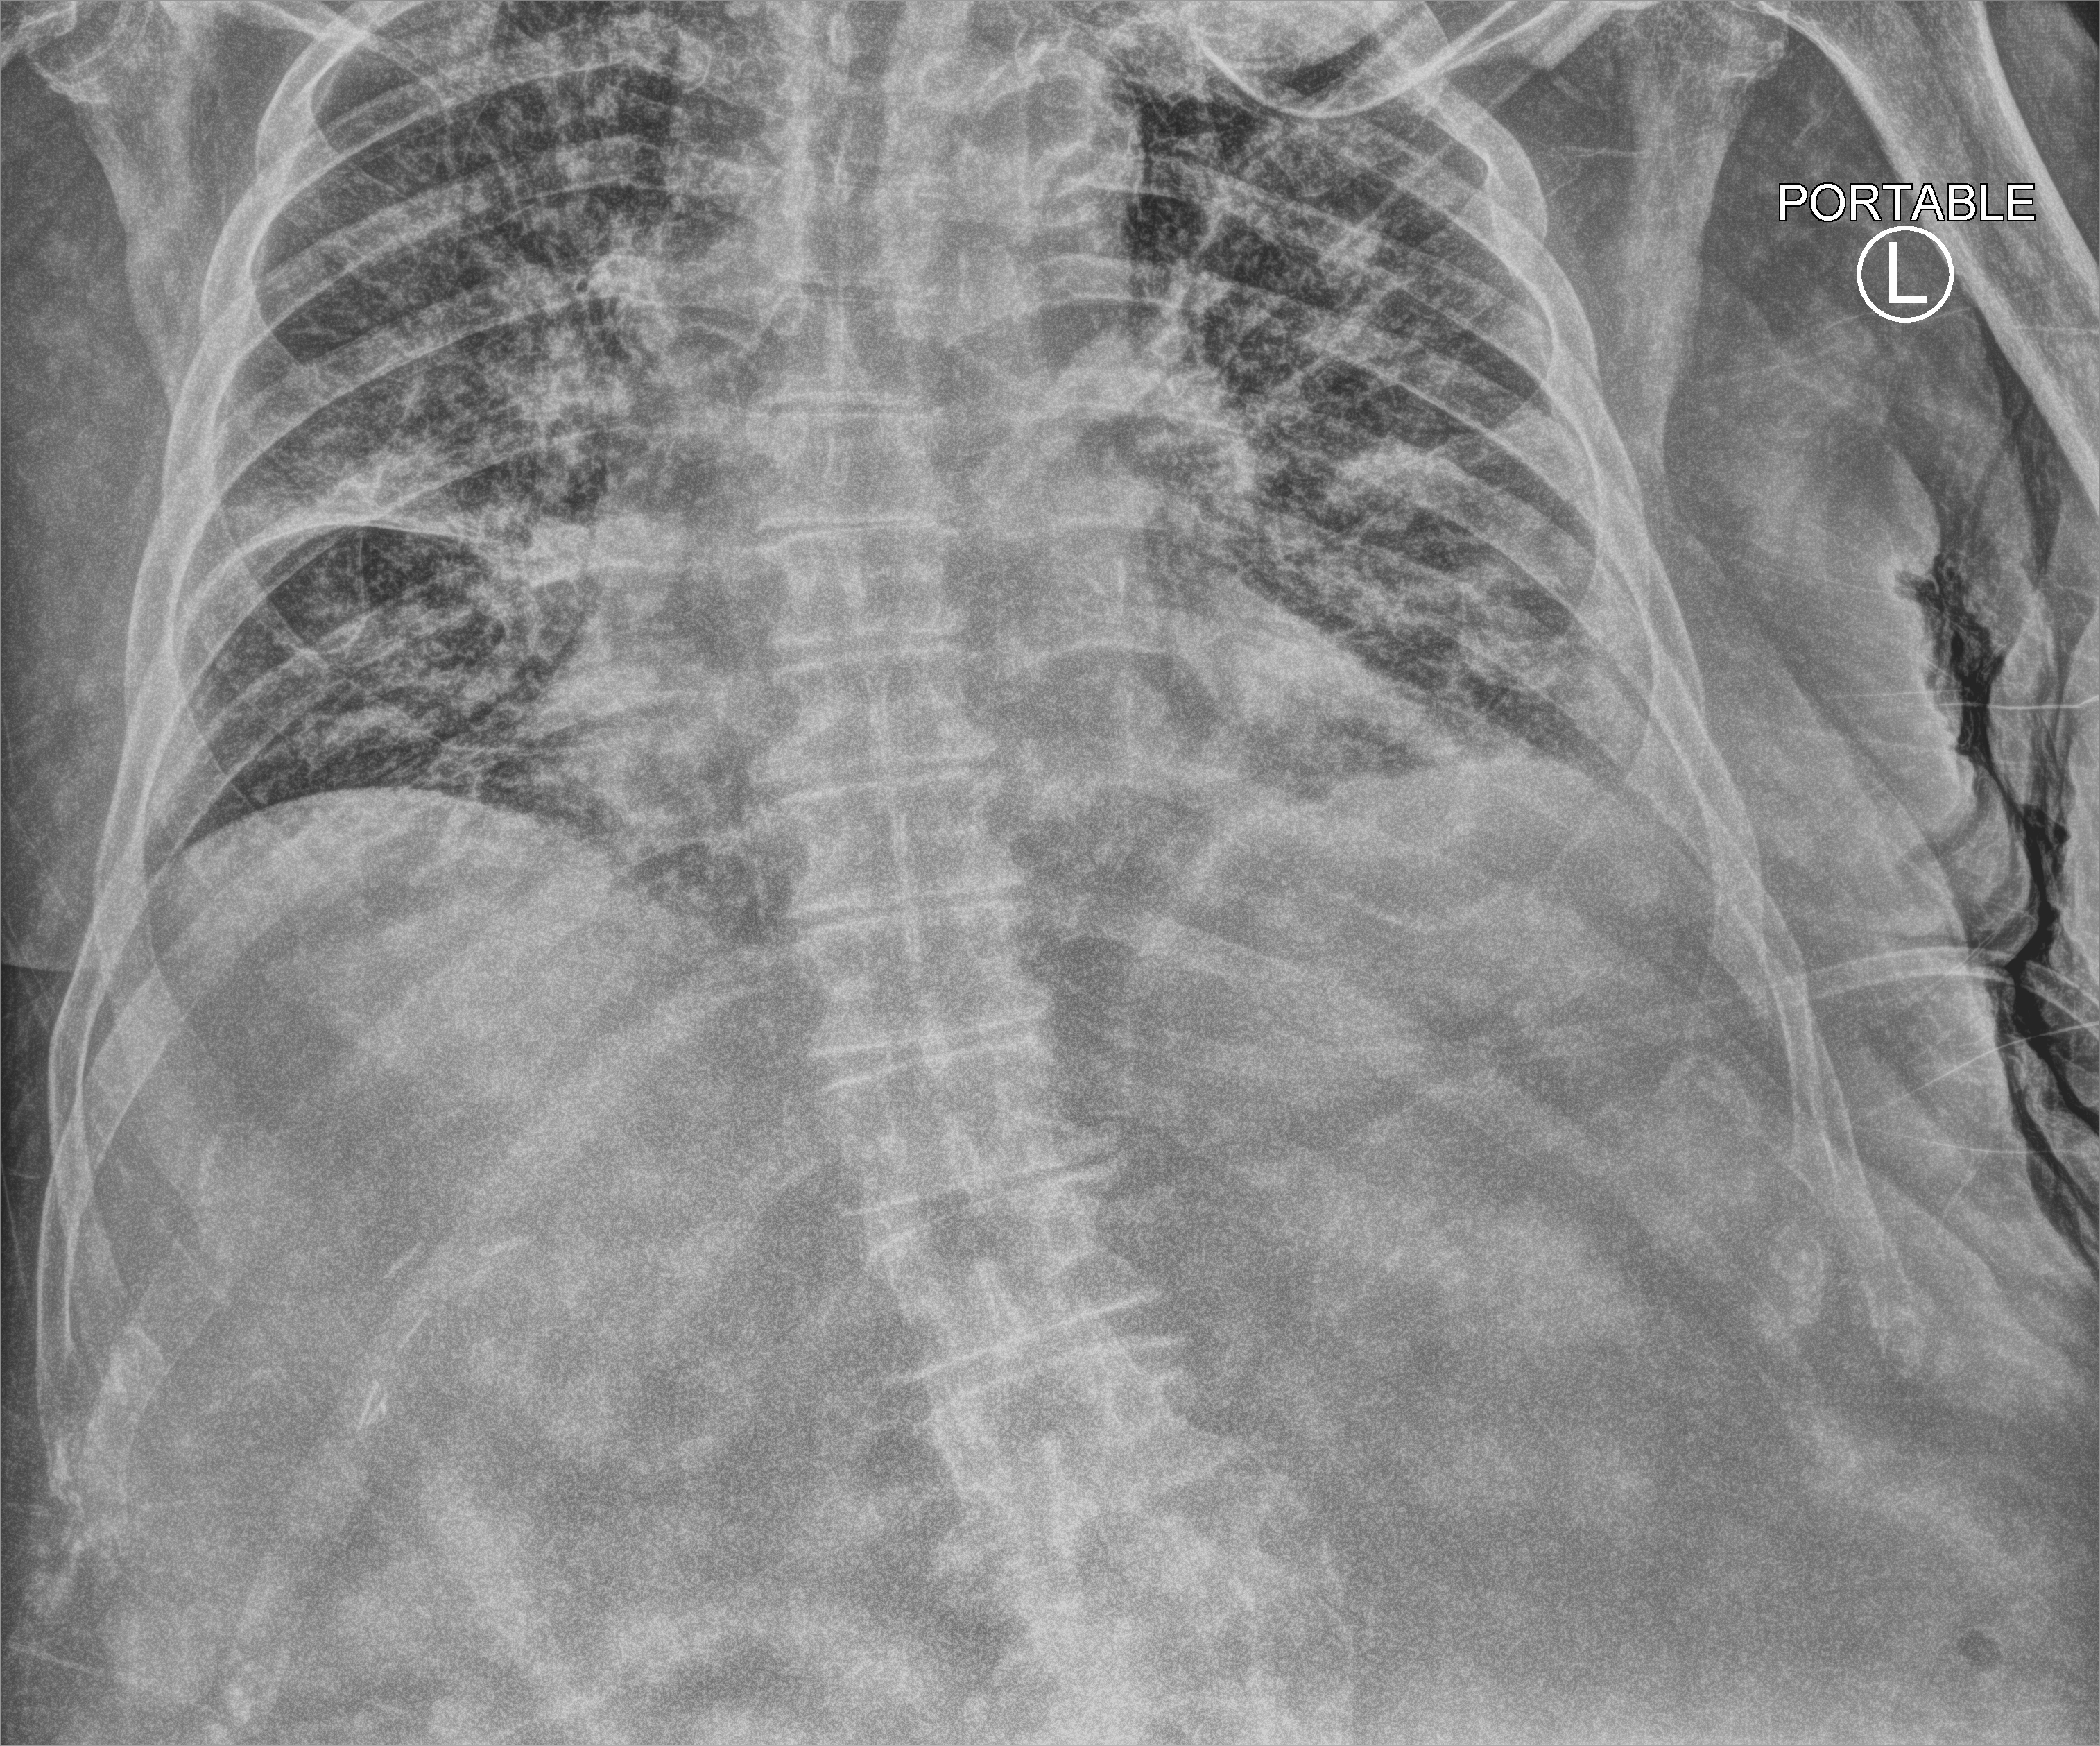
Chest X-ray (portable), anteroposterior (AP) projection. Patient hospitalised with COVID-19; male, aged 75–90 years.
Admission-level facts for this patient (not findings on this image; timing relative to this image not recorded):
- admitted to intensive care during this hospital stay: no
- other chronic lung disease (admission record): no